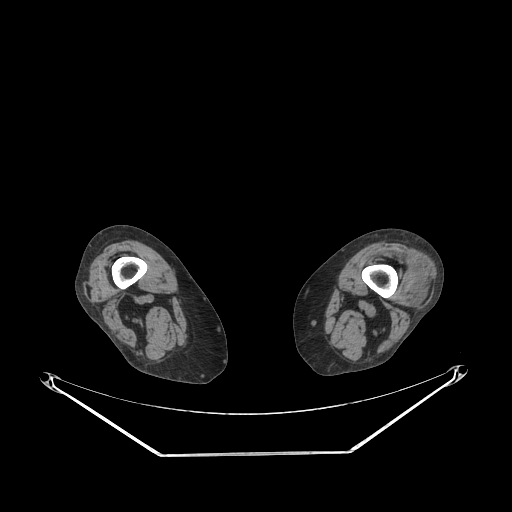
CT of an extremity soft-tissue mass (from a PET/CT study), one axial slice. Slice 189 of 267 in the series (ordered by position). Soft-tissue window (W 400 / L 40 HU). 3.75 mm slice thickness. 512 × 512 image matrix, field of view 500 × 500 mm. Female patient. From the clinical record (not read from this slice): histological type: undifferentiated – high grade; grade: high; site of the primary tumour: left thigh.
Structures marked on this image (expert contour drawn on MRI and transferred to this co-registered scan by the dataset authors):
- gross tumour volume including surrounding oedema: bounding box <406,279,417,289> (left, top, right, bottom; pixels)